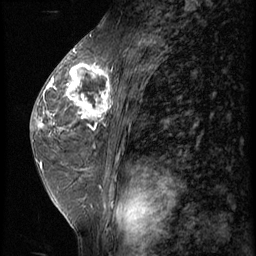
Breast MRI (dynamic contrast-enhanced), one sagittal slice; position 34 of 62 along the scan axis; 3 images stored at this slice position (order not interpretable as contrast timing); 1.5 T; TE 4.2 ms, TR 9 ms; 2.5 mm slice thickness; 256 × 256 image matrix, field of view 180 × 180 mm. Patient: female, 44 years. From the clinical record (not read from this slice): setting: breast cancer imaged before/during neoadjuvant chemotherapy; receptor status: triple-negative.
Annotated regions visible in this slice (semi-automatically segmented with operator editing):
- analysis volume of interest (the breast-tissue region the enhancement analysis was run in; not a lesion): bounding box <67,64,116,125> (left, top, right, bottom; pixels)
- tumour enhancement mask (voxels above the 140 % enhancement threshold inside the analysis volume of interest): <67,64,116,125>